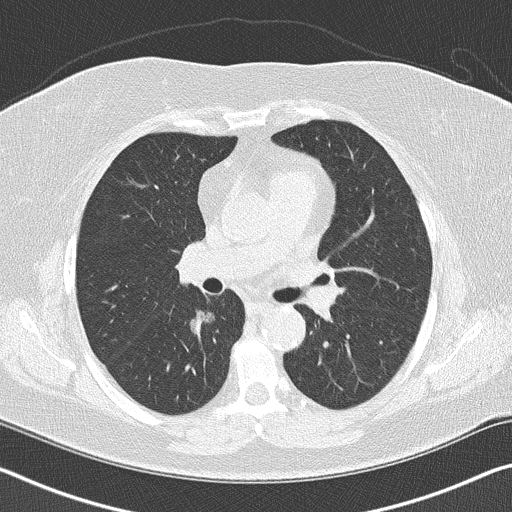
Axial slice from a low-dose chest CT screening exam, first (baseline) screen, lung window (W 1500 / L -600 HU), 2 mm slice thickness, lung (sharp) reconstruction kernel (B50f), 512 × 512 image matrix. Female participant, aged 60 years at enrolment. Former smoker at enrolment.
Lesion marked by an expert reader, bounding box [x1, y1, x2, y2] px = [174, 296, 227, 346]. The screening reader recorded 2 non-calcified nodules or masses ≥4 mm on this exam (right lower lobe, left upper lobe); which of them this box marks is not recorded. Lung cancer was diagnosed 482 days after this screen (after the second annual screen): bronchiolo-alveolar carcinoma, non-mucinous, right lower lobe, stage IA (AJCC 6th edition), 15 mm at pathology.